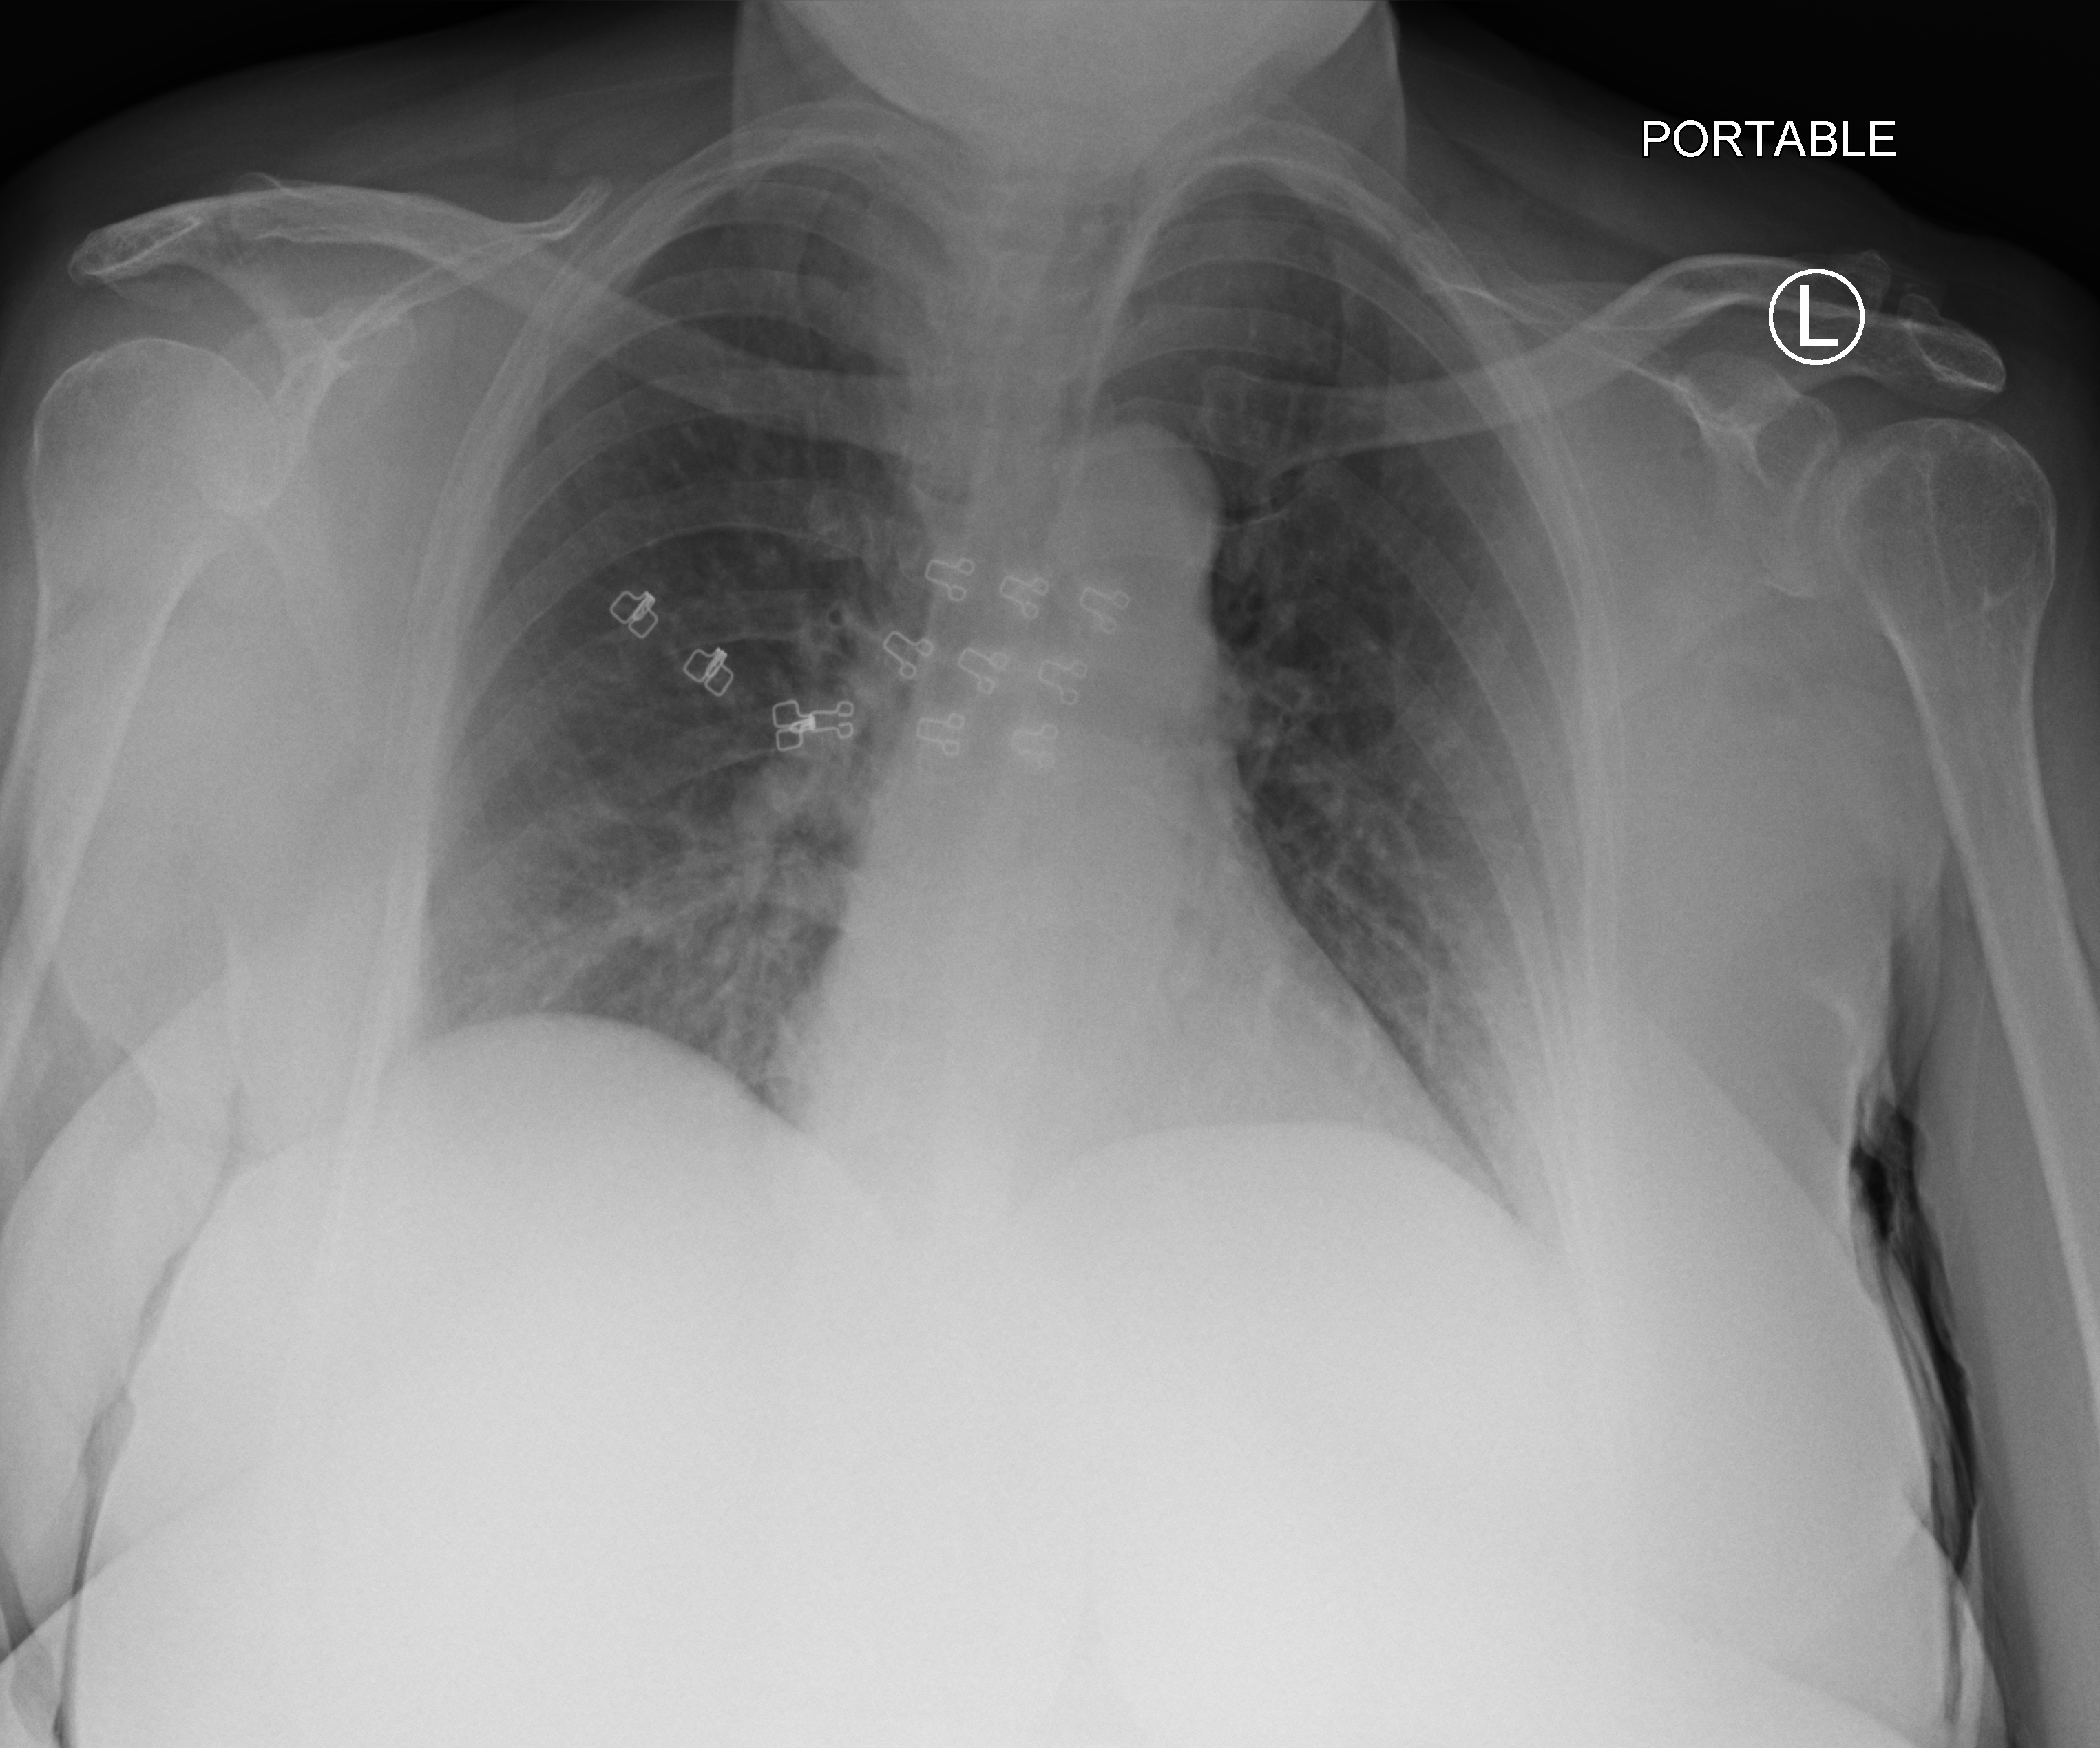
Bedside chest radiograph (computed radiography). Patient hospitalised with COVID-19; female, aged 60–74 years.
Admission-level facts for this patient (not findings on this image; timing relative to this image not recorded): mechanically ventilated during this hospital stay: no; admitted to intensive care during this hospital stay: no.